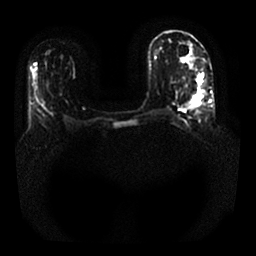
Breast MRI, one axial slice; position 9 of 25 along the scan axis; diffusion-weighted series; image 2 of 4 stored at this slice position (different b-values; order by instance number); 1.5 T; 256 × 256 image matrix. Female patient.
Outlined on this slice (outlined manually by an expert reader):
- tumour on diffusion-weighted imaging: bounding box [x1, y1, x2, y2] px = [197, 75, 203, 82]